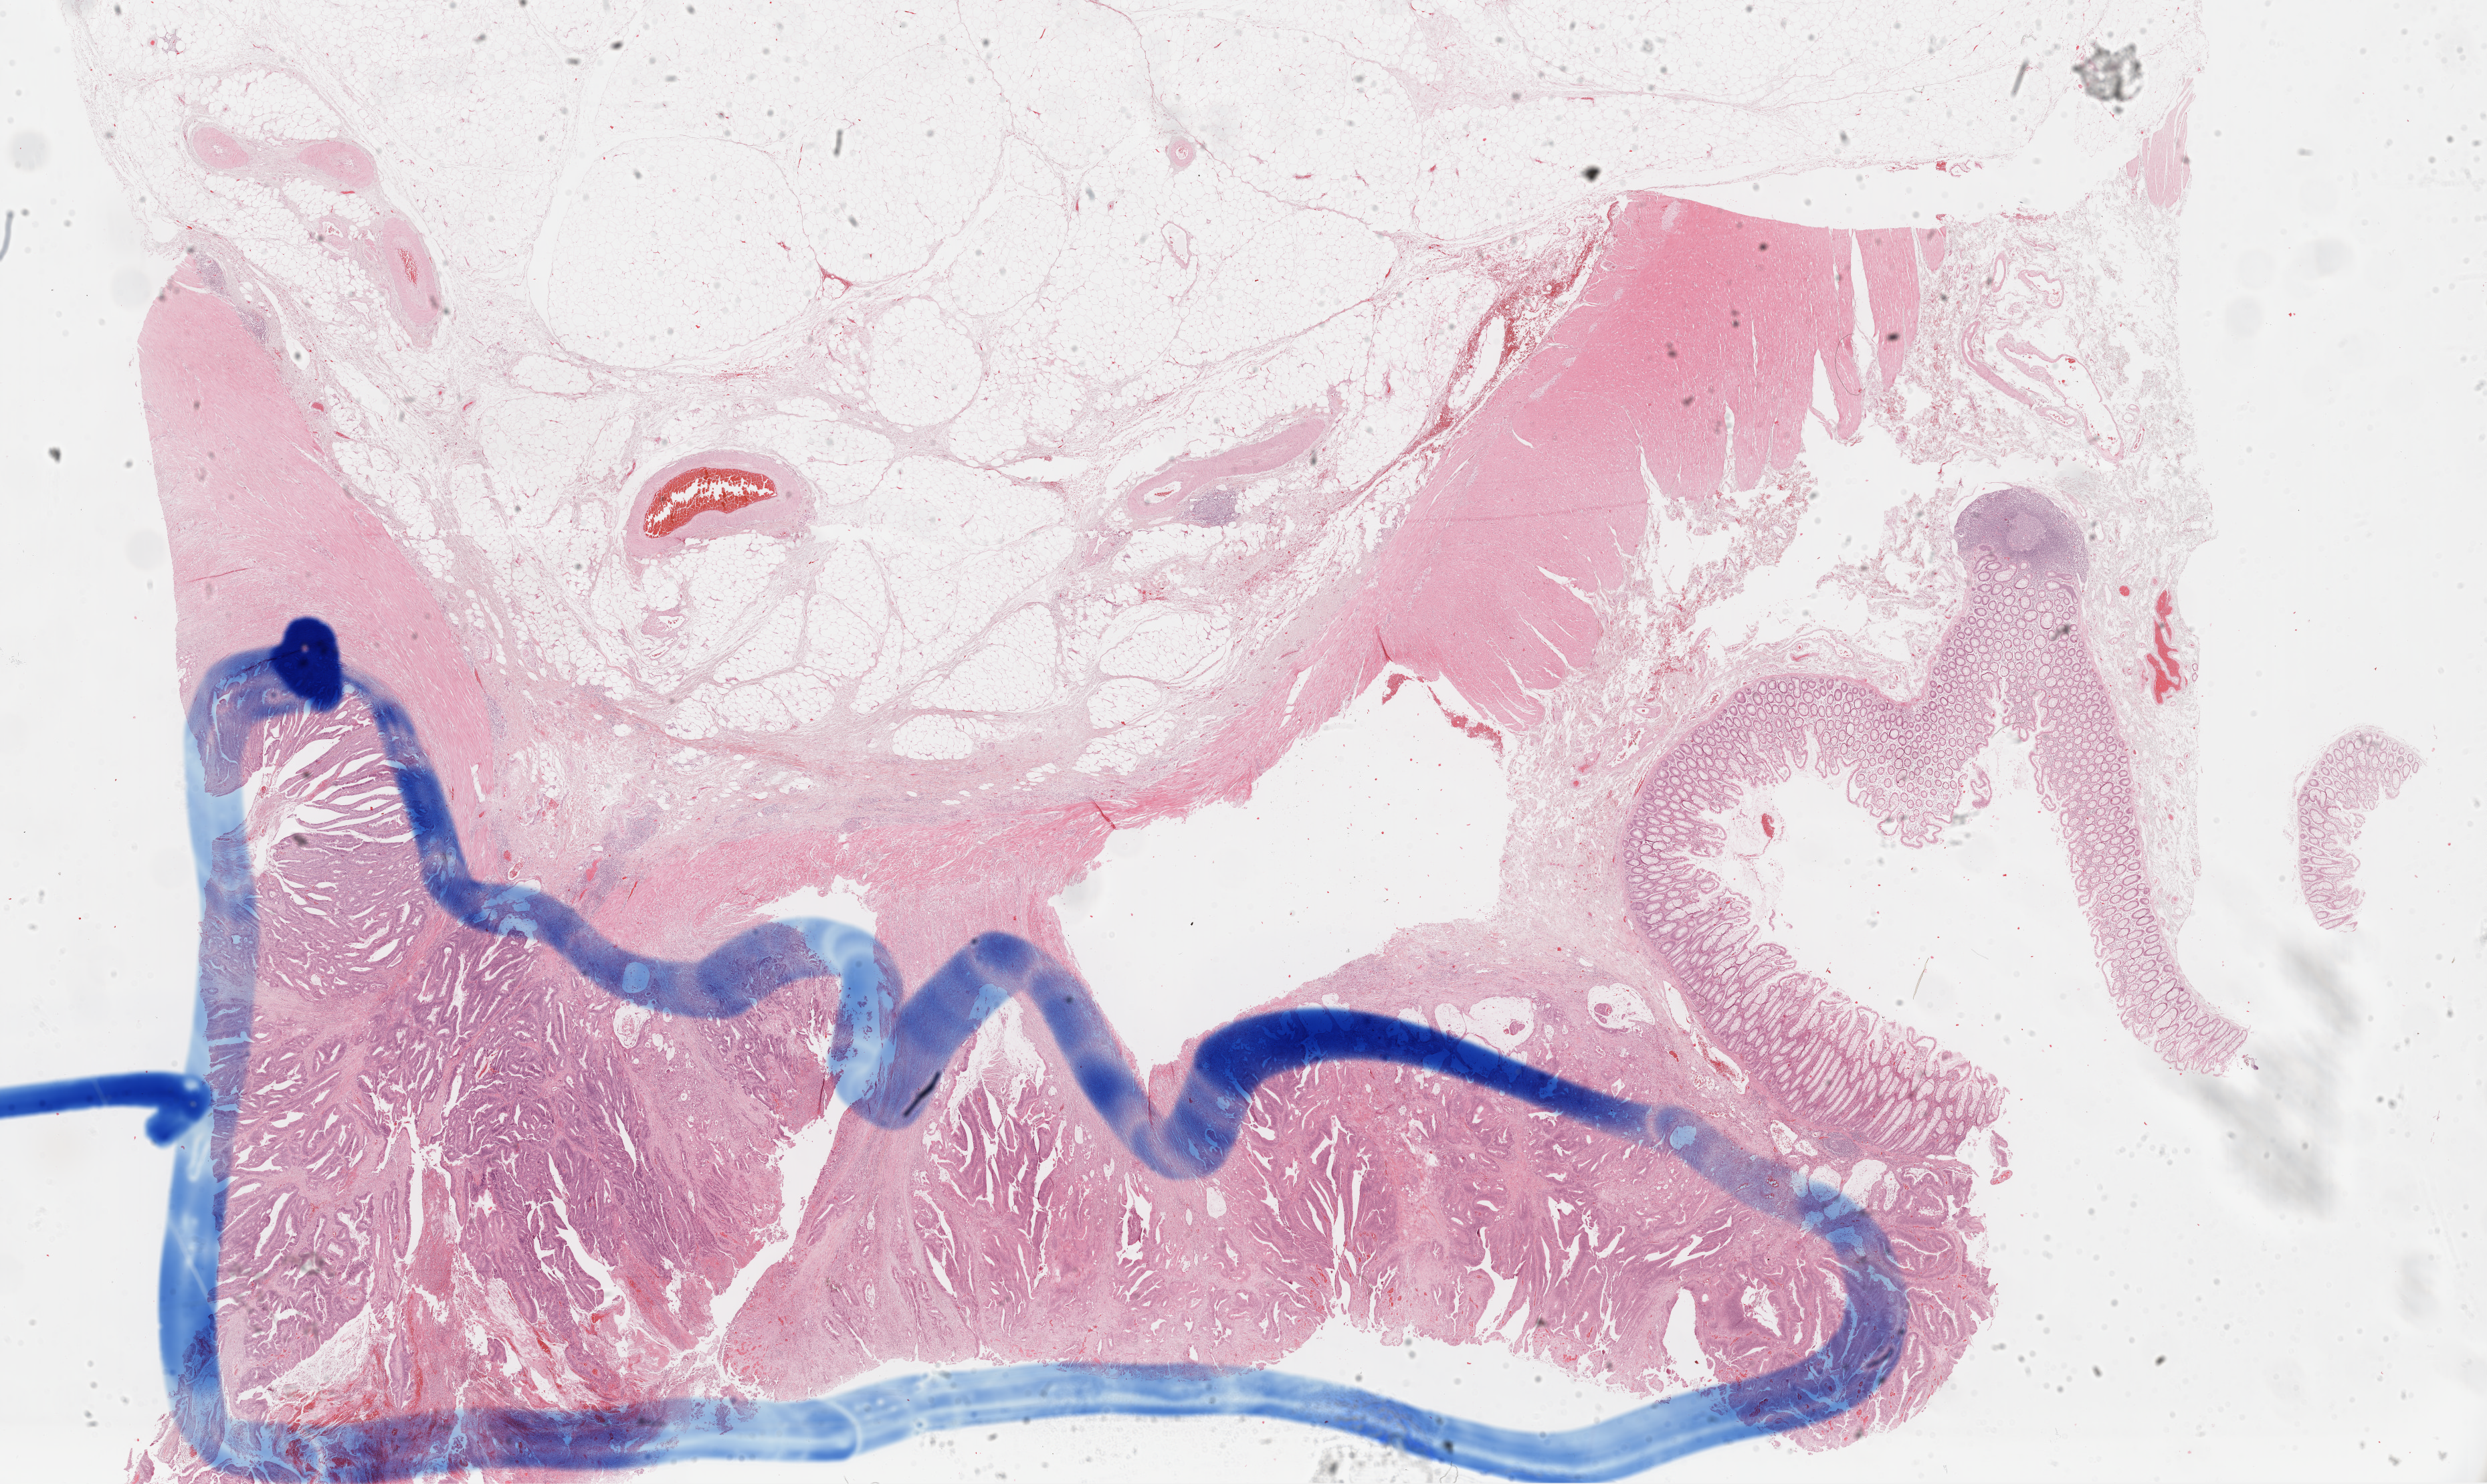
Hematoxylin and eosin (H&E) stained whole-slide image — shown as a low-resolution overview of the whole scanned area (about 29.4 x 17.5 mm). Formalin-fixed paraffin-embedded (FFPE) diagnostic section. Primary tumour sample from the colon. Patient: male, age at initial diagnosis 63 years.
AJCC pathologic stage: IIA (6th edition). Pathologic diagnosis: Adenocarcinoma, NOS.